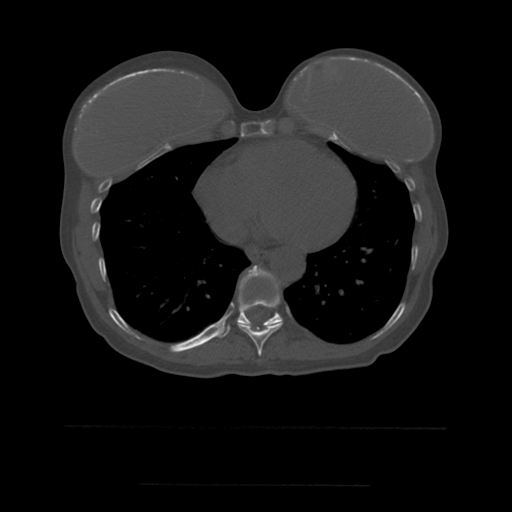
CT including the spine, one axial slice. Slice 313 of 544 in the series (ordered by position). Bone window (W 1800 / L 400 HU). 1.25 mm slice thickness. 512 × 512 image matrix, field of view 350 × 350 mm. Patient age 58 years. Case-level facts recorded for this patient, not image findings: primary cancer: lung.
Outlined on this slice (semi-automatic segmentation, software-assisted and operator-edited):
- T10 vertebra: bounding box <217,288,283,338> (left, top, right, bottom; pixels)
- T9 vertebra: <237,266,283,356>